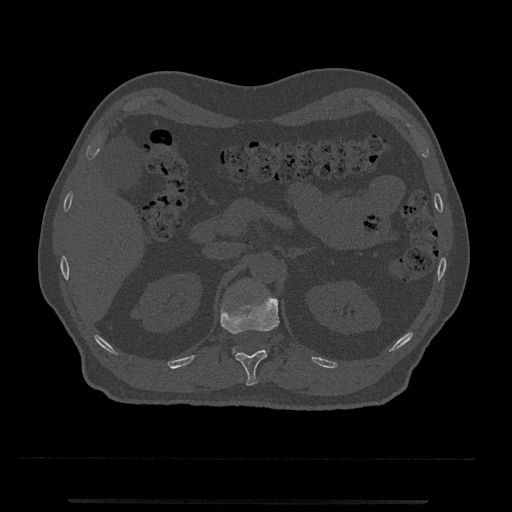
CT including the spine, one axial slice; position 380 of 797 along the scan axis; bone window (W 1800 / L 400 HU); 0.5 mm slice thickness; 512 × 512 image matrix. Patient: male, 63 years. Case-level facts recorded for this patient, not image findings: primary cancer: prostate.
Annotated regions visible in this slice (semi-automatically segmented with operator editing):
- L1 vertebra: bounding box (x1, y1, x2, y2) in pixels: (232, 348, 236, 354)
- T12 vertebra: (220, 293, 280, 386)